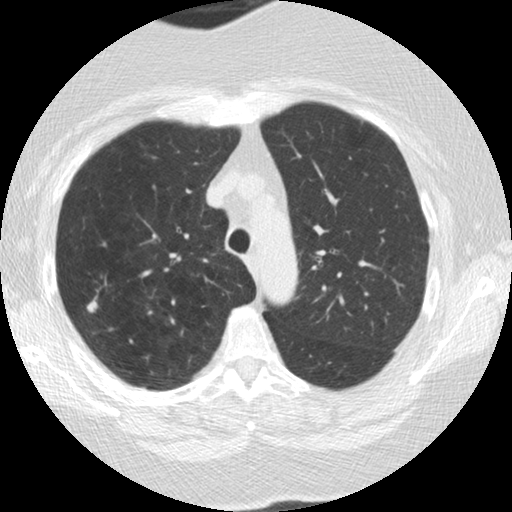
Low-dose screening chest CT, one axial slice. Slice 130 of 166 in the series (ordered by position). Reconstruction kernel STANDARD. 120 kVp. Lung window (W 1500 / L -600 HU). 2.5 mm slice thickness. 512 × 512 image matrix, field of view 309 × 309 mm.
Structures marked on this image (manually delineated by an expert):
- lesion 1 (tumor, upper lobe of right lung): bounding box [x1, y1, x2, y2] px = [87, 300, 98, 313]